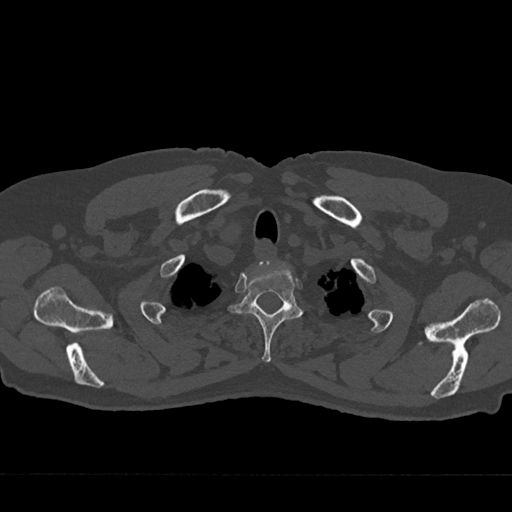
CT including the spine, one axial slice. Position 616 of 797 along the scan axis. 120 kVp. Bone window (W 1800 / L 400 HU). 0.5 mm slice thickness. 512 × 512 image matrix, field of view 377 × 377 mm. Patient: male, 75 years. Case-level facts recorded for this patient, not image findings: primary cancer: renal; vertebrae with lytic lesions (as recorded): T4.
Outlined on this slice (semi-automatic segmentation, software-assisted and operator-edited):
- T1 vertebra: bounding box <261,261,269,262> (left, top, right, bottom; pixels)
- T2 vertebra: <228,261,303,362>